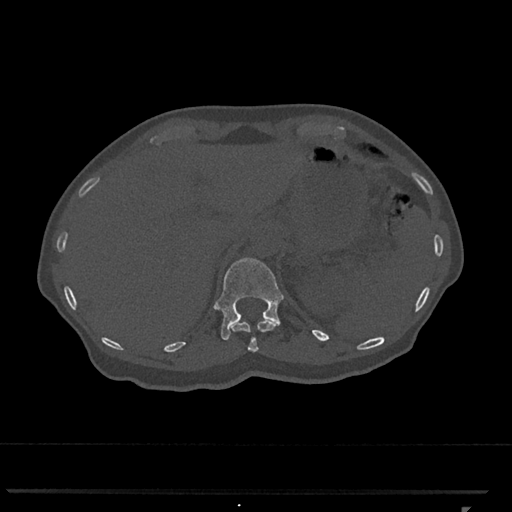
CT including the spine, one axial slice. Reconstruction kernel Br40s/3. 120 kVp. Bone window (W 1800 / L 400 HU). 0.5 mm slice thickness. 512 × 512 image matrix, field of view 380 × 380 mm. Patient: female, 62 years. Case-level facts recorded for this patient, not image findings: primary cancer: renal.
Structures marked on this image (semi-automatically segmented with operator editing):
- T11 vertebra: bounding box [x1, y1, x2, y2] px = [231, 319, 277, 352]
- T12 vertebra: [214, 258, 284, 340]